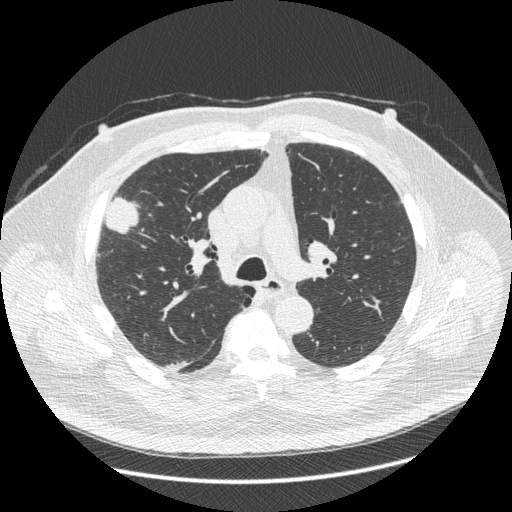
Low-dose screening chest CT, one axial slice. Position 280 of 426 along the scan axis. Reconstruction kernel STANDARD. Lung window (W 1500 / L -600 HU). 1.25 mm slice thickness. 512 × 512 image matrix.
Outlined on this slice (expert manual segmentation):
- lesion 1 (tumor, upper lobe of right lung): bounding box [x1, y1, x2, y2] px = [106, 197, 138, 233]